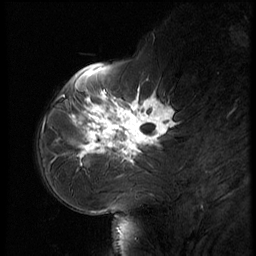
Breast MRI (dynamic contrast-enhanced), one sagittal slice; position 20 of 56 along the scan axis; dynamic contrast-enhanced series, image 2 of 3 at this slice position (ordered by acquisition); 1.5 T; TE 4.2 ms, TR 9 ms; 2.5 mm slice thickness; 256 × 256 image matrix, field of view 180 × 180 mm. Female patient, age 61 years. Case-level facts recorded for this patient, not image findings: setting: breast cancer imaged before/during neoadjuvant chemotherapy; receptor status: HR-positive, HER2-negative.
Annotated regions visible in this slice (semi-automatic segmentation, software-assisted and operator-edited):
- analysis volume of interest (the breast-tissue region the enhancement analysis was run in; not a lesion): box from (x=65, y=74) to (x=185, y=175) px
- tumour enhancement mask (voxels above the 140 % enhancement threshold inside the analysis volume of interest): (x=72, y=88)–(x=175, y=166)